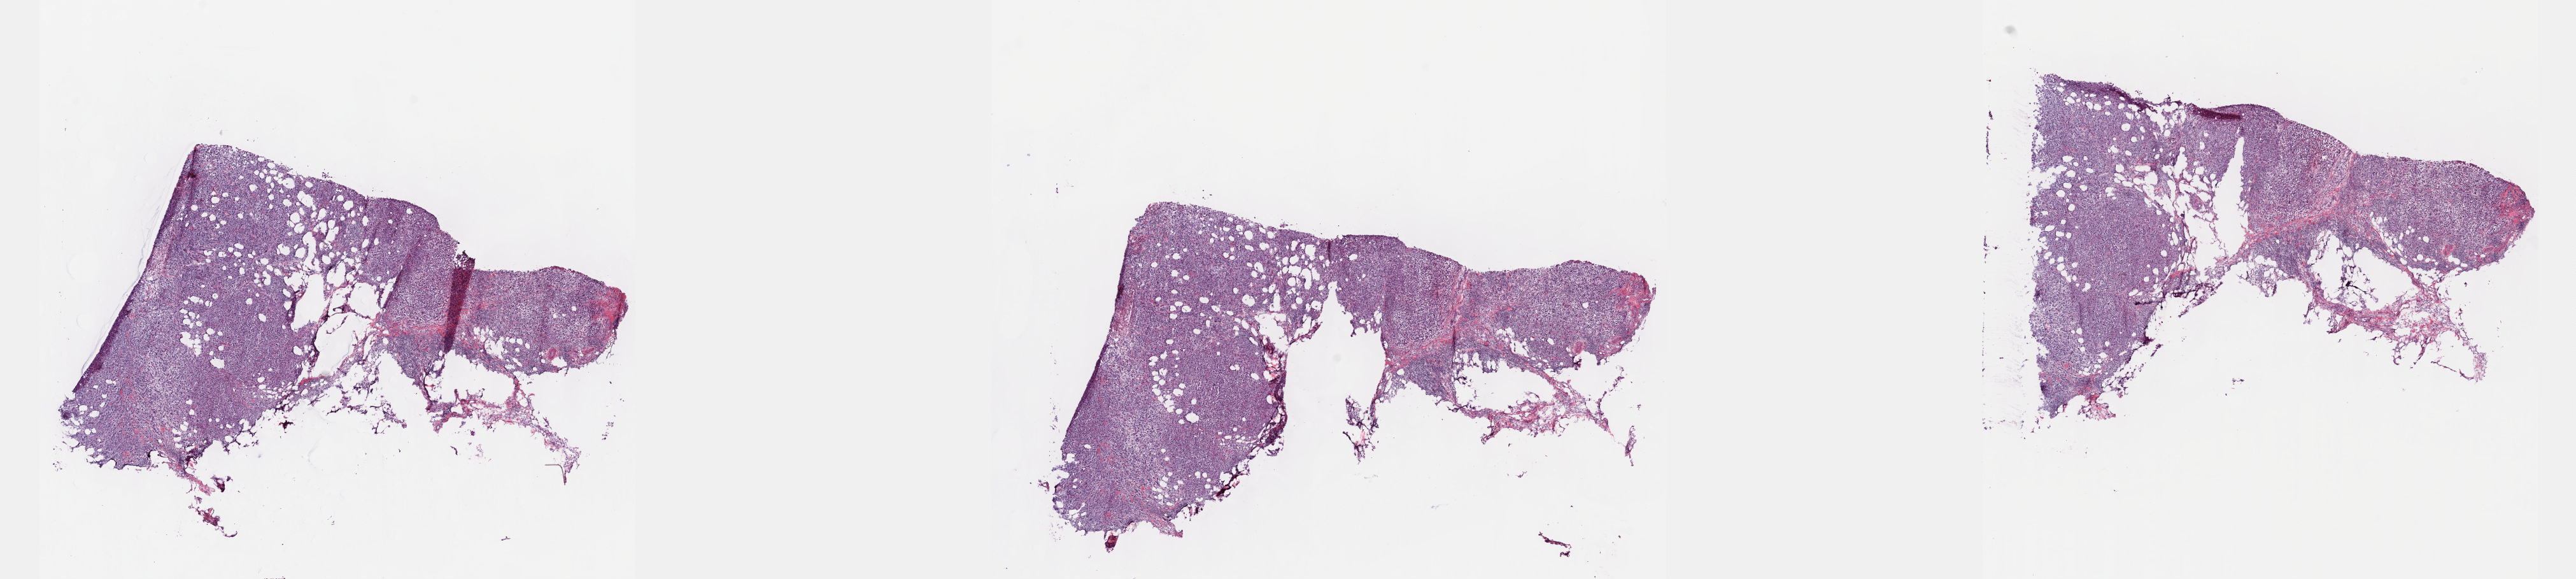
Whole-slide histology image, H&E — low-resolution overview of the scanned area, about 32.7 x 7.3 mm. Frozen section from the top of the tissue portion. Metastatic tumour sample, sampled site not recorded. Female, age 63 years at initial diagnosis. Slide review estimates, as recorded: tumour cells 95%, tumour nuclei 98%, normal cells 5%, stromal cells 0%, necrosis 0%. Infiltration values recorded for this section: lymphocyte infiltration 0%, monocyte infiltration 0%, neutrophil infiltration 0%.
This section: metastatic tumour tissue. Patient diagnosis: Malignant melanoma, NOS.